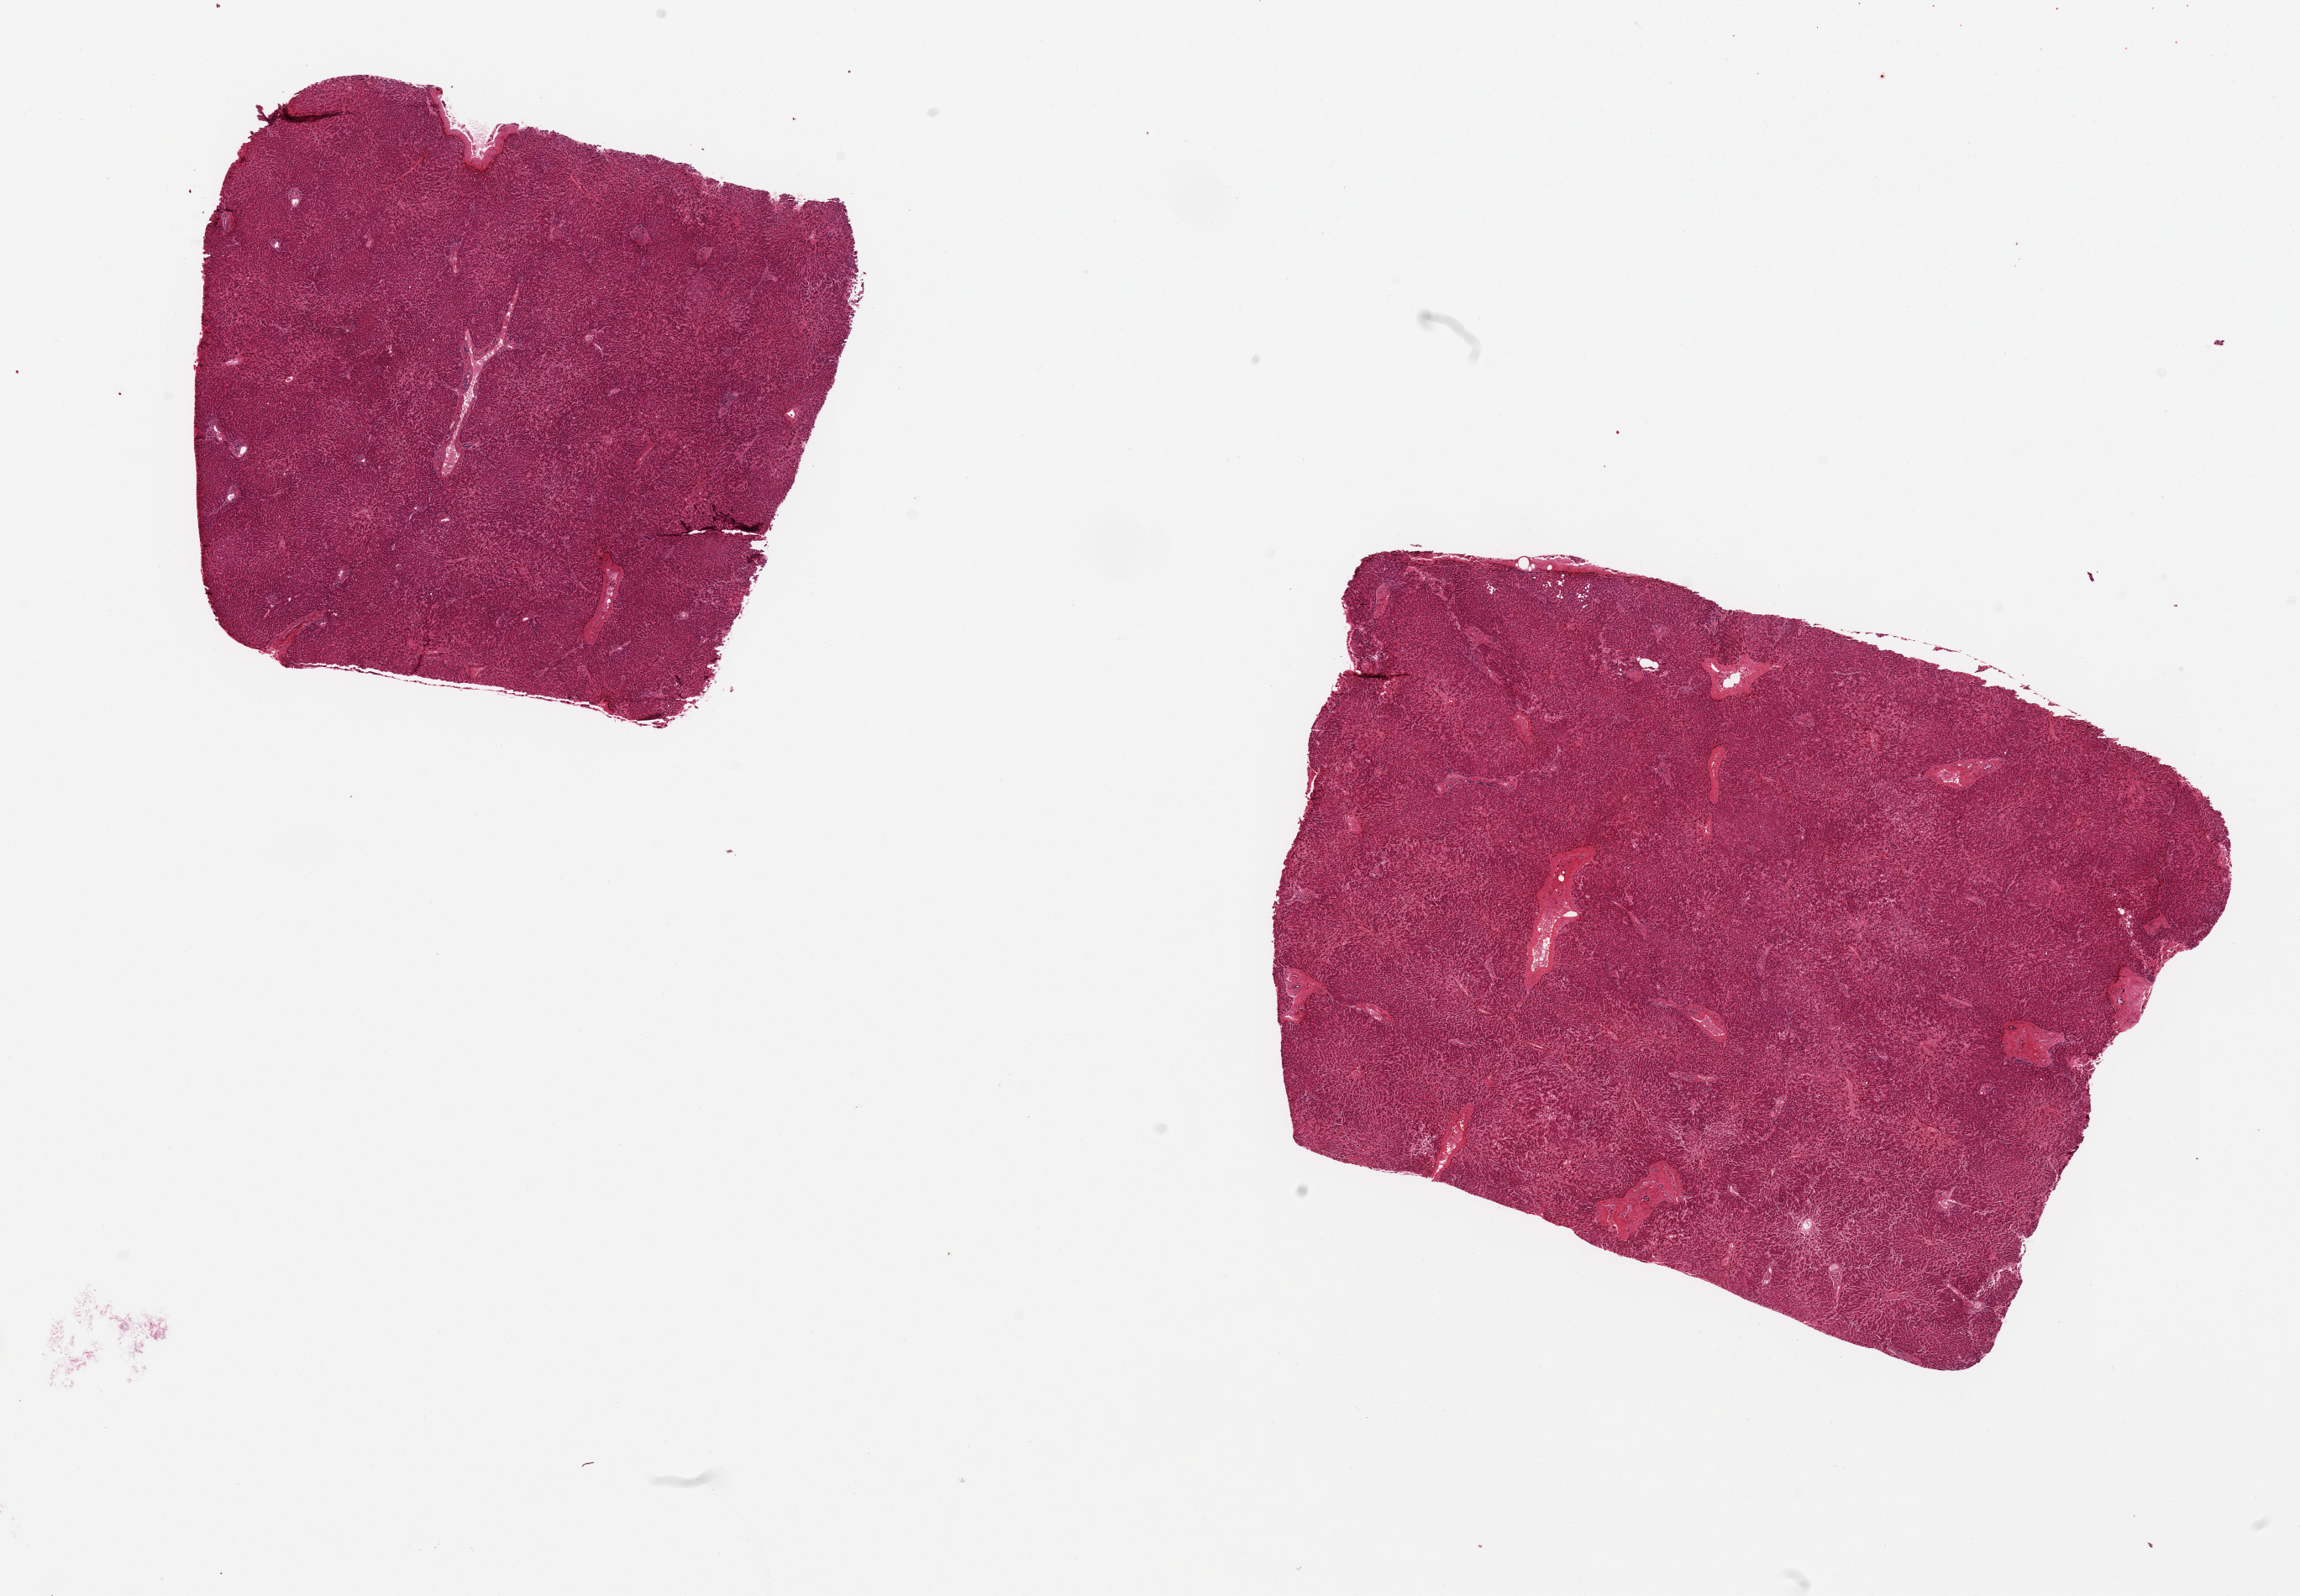
Digitized haematoxylin and eosin-stained section, shown as a low-resolution overview of the whole scanned area (about 21.7 x 15.0 mm), PAXgene-fixed paraffin-embedded (PFPE) section, sampled site (target tissue): liver, tissue donor sample. Donor: male.
Reviewer comment on this tissue sample: 2 aliquots, ~7x6mm. Fairly well preserved, minimal fat.